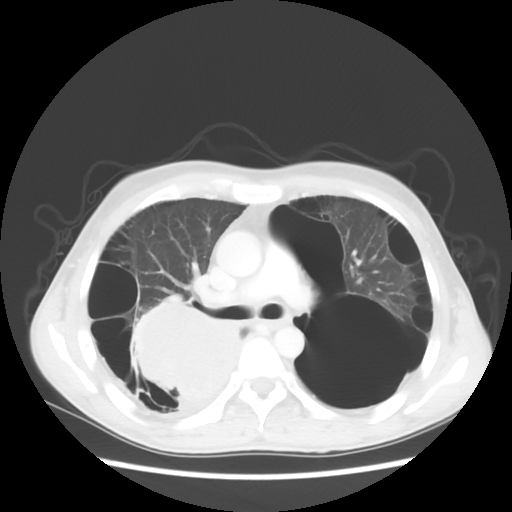
Chest CT, one axial slice; slice 34 of 56 in the series (ordered by position); reconstruction kernel STANDARD; 140 kVp; lung window (W 1500 / L -600 HU); 512 × 512 image matrix. Male patient, age 41 years. From the clinical record (not read from this slice): clinical TNM (as recorded): T4 N0 M1a.
Outlined on this slice (bounding box drawn by a radiologist):
- lung tumour (recorded histology: large cell carcinoma): bounding box (x1, y1, x2, y2) in pixels: (122, 287, 250, 418)